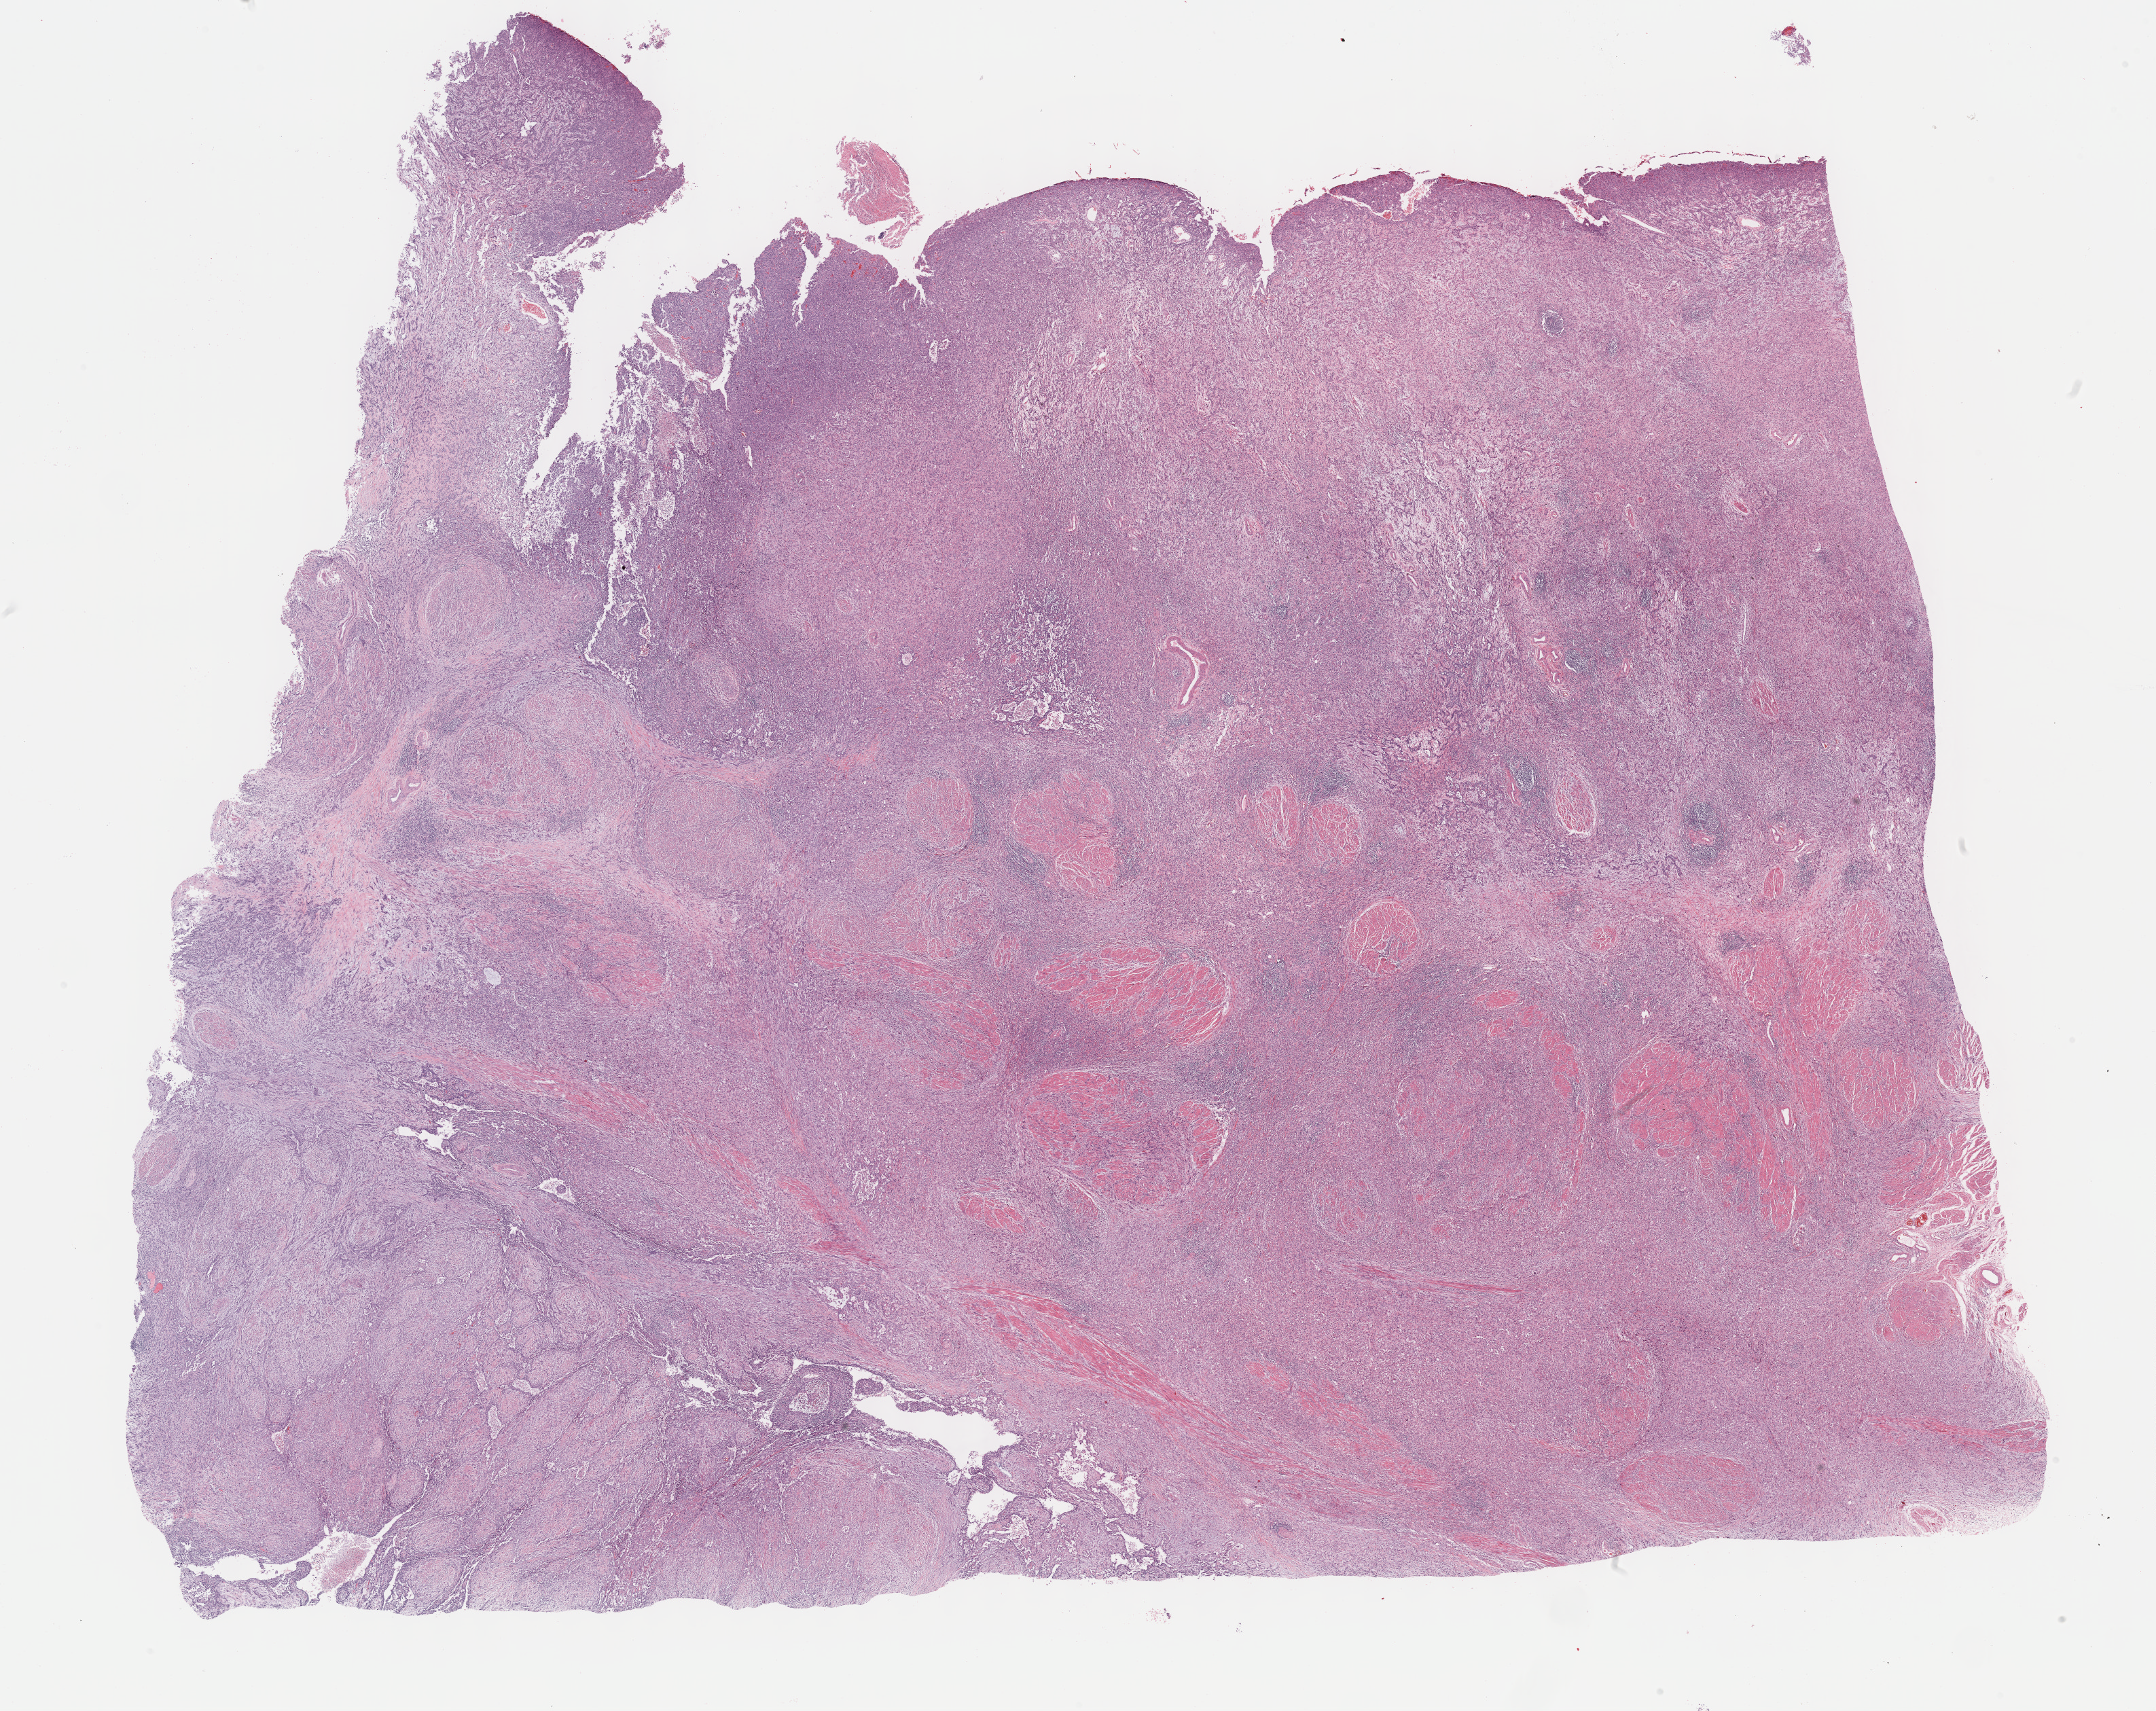
Whole-slide histology image, Hematoxylin and eosin (H&E) stained — whole scanned area (about 25.7 x 20.4 mm, acquisition: 40x scan) shown as a low-resolution overview; formalin-fixed paraffin-embedded (FFPE) diagnostic section; sample: primary tumour, bladder. Female, age 77 years at initial diagnosis. Histologic grade: high grade.
- AJCC pathologic stage: III (6th edition)
- pathologic diagnosis: Transitional cell carcinoma